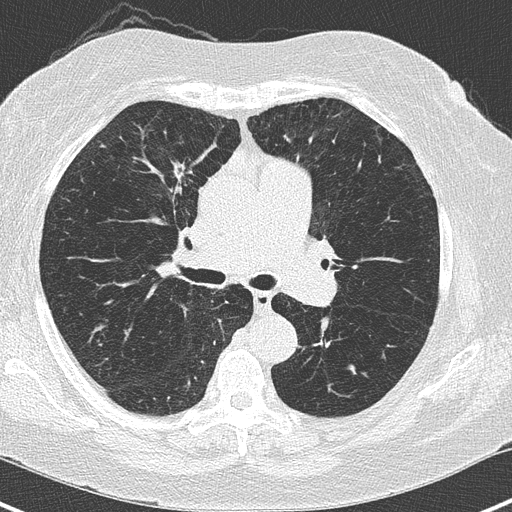
Axial slice from a low-dose chest CT screening exam; third screening round (two years after baseline); lung window (W 1500 / L -600 HU); 120 kVp. Female participant, aged 62 years at enrolment. Current smoker at enrolment.
Lesion marked by an expert reader, bounding box (x1, y1, x2, y2) in pixels: (147, 150, 210, 207). The screening reader recorded 4 non-calcified nodules or masses ≥4 mm on this exam (right upper lobe, left lower lobe, left lower lobe); which of them this box marks is not recorded. Participant outcome: lung cancer diagnosed 41 days after this screen — adenocarcinoma, NOS, right upper lobe, moderately differentiated (G2), stage IA (AJCC 6th edition), 15 mm at pathology.